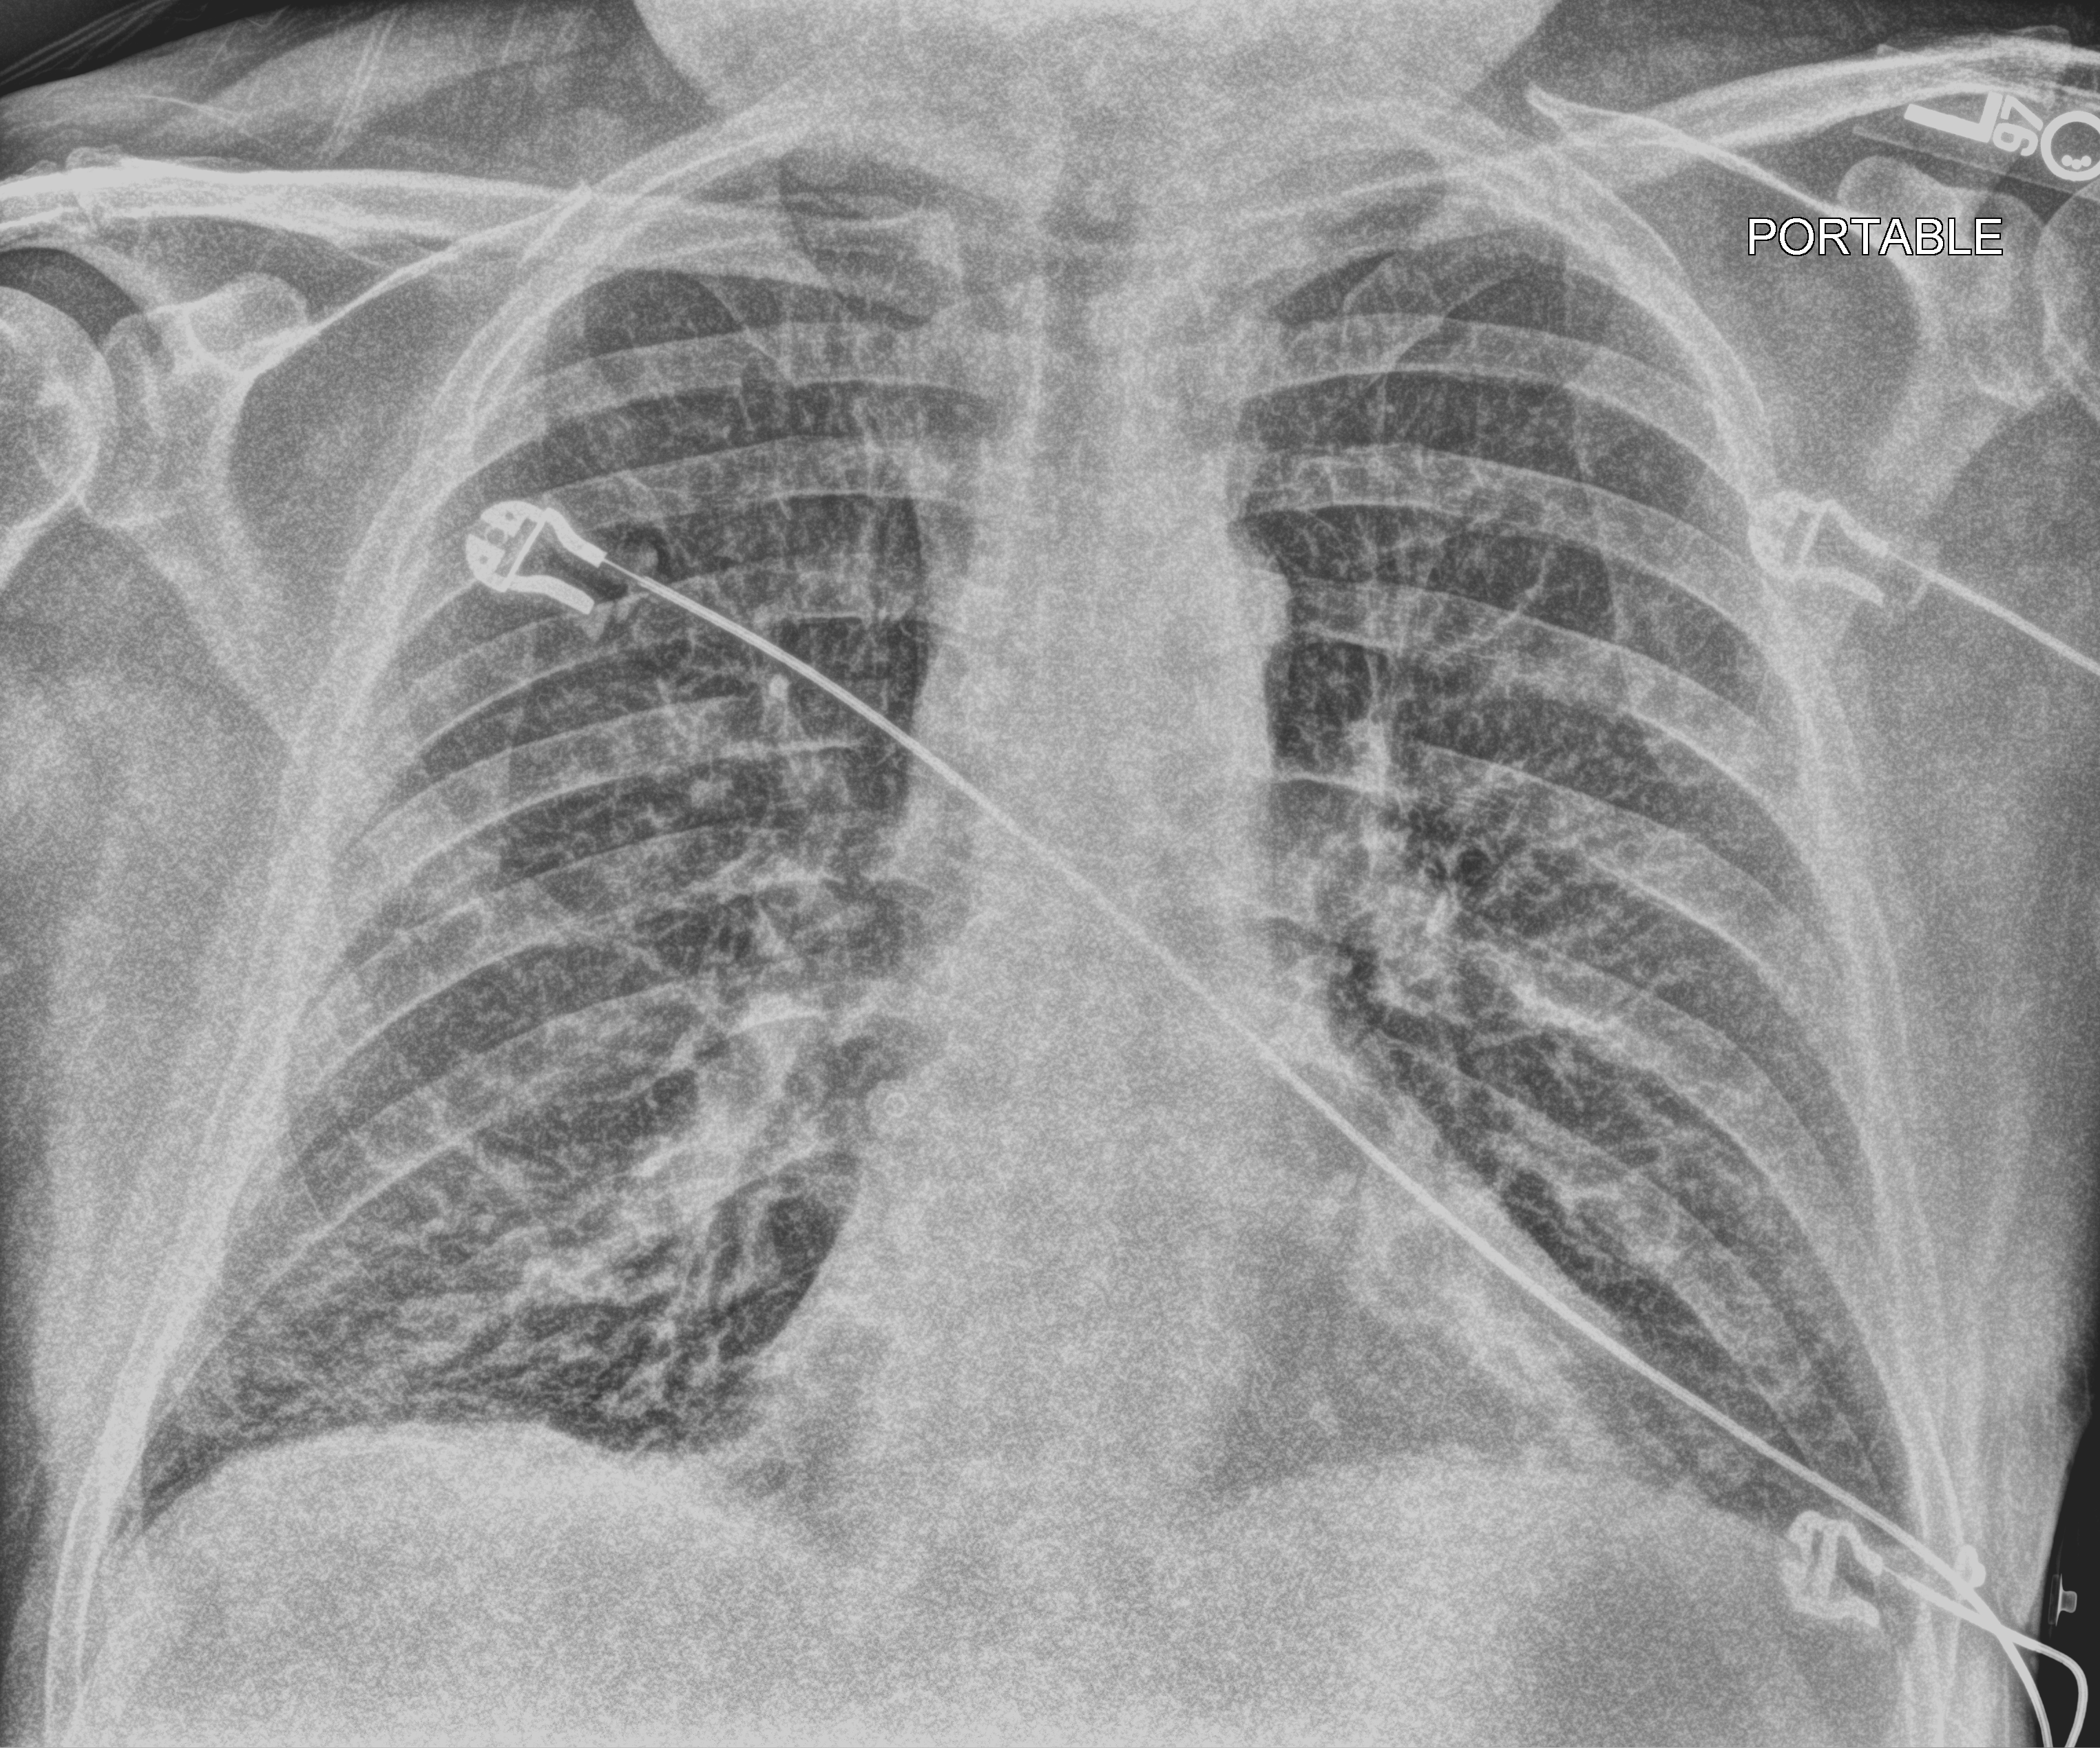
Bedside chest radiograph (computed radiography), anteroposterior (AP) projection. Adult patient hospitalised with COVID-19, age 18–59 years.
Admission-level facts for this patient (not findings on this image; timing relative to this image not recorded): length of hospital stay: 3 days; other chronic lung disease (admission record): yes; mechanically ventilated during this hospital stay: no.